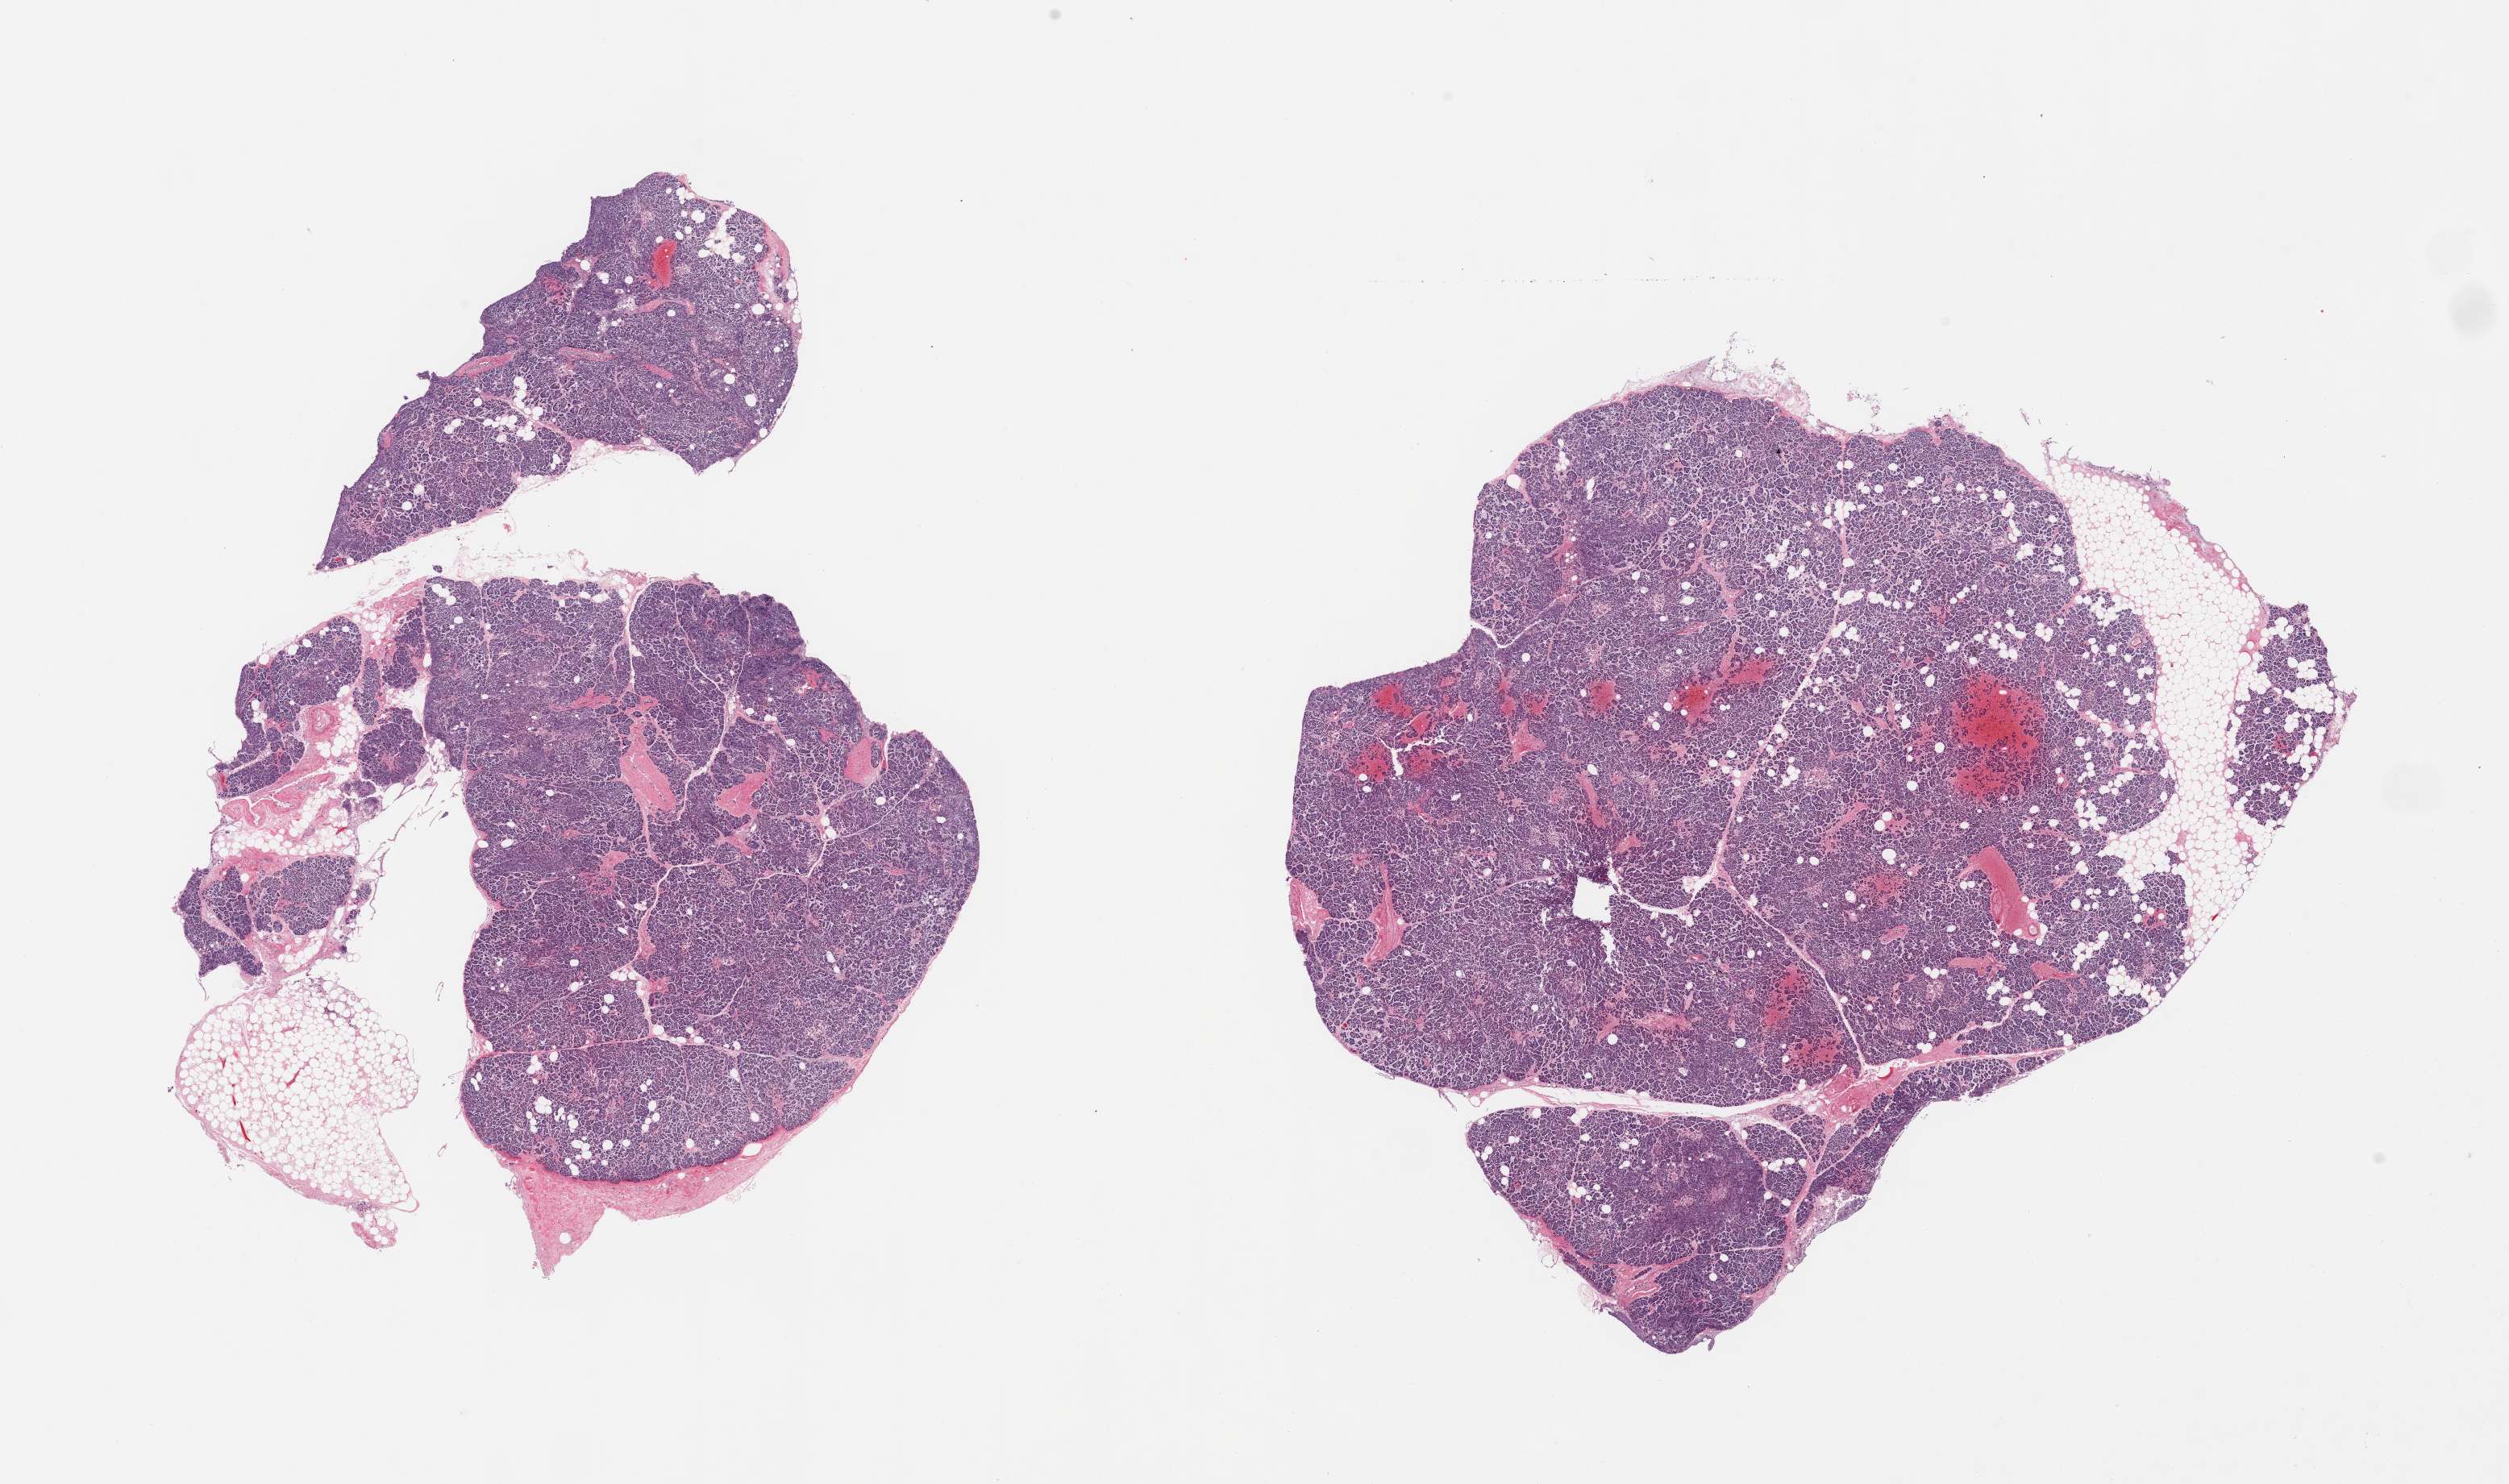
Haematoxylin and eosin whole-slide image, brightfield, whole scanned area (about 24.6 x 14.6 mm, from a 20x scan) shown as a low-resolution overview. PAXgene-fixed paraffin-embedded (PFPE) section. Target tissue: pancreas. Tissue donor sample. Donor: male.
Review note (as recorded): 2 pieces, moderately advanced saponification, Islets visible but fairly advanced degradation.